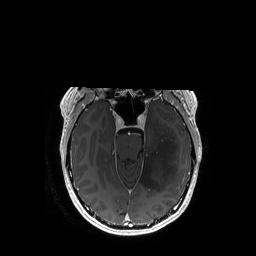
Brain MRI from a brain-tumour surgery series, one axial slice. Slice 112 of 192 in the series (ordered by position). T1-weighted post-contrast. 1 mm slice thickness. 256 × 256 image matrix. From the clinical record (not read from this slice): histopathology: Astrocytoma; WHO grade: 3; IDH mutation: yes; tumour location: Left Temporal.
Annotated regions visible in this slice (manually delineated by an expert):
- tumour: bounding box (x1, y1, x2, y2) in pixels: (140, 121, 178, 191)